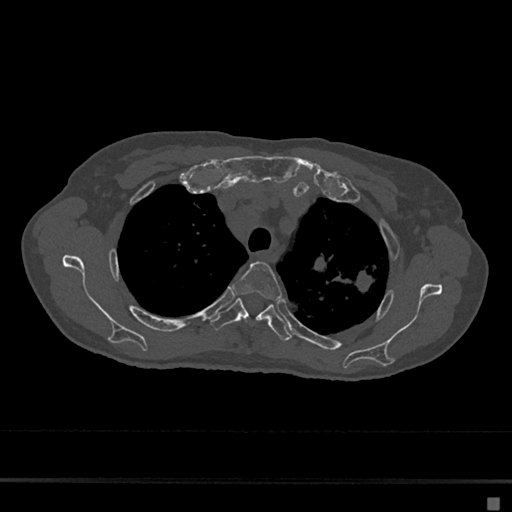
CT including the spine, one axial slice; slice 520 of 797 in the series (ordered by position); 120 kVp; bone window (W 1800 / L 400 HU); 512 × 512 image matrix, field of view 360 × 360 mm. Female patient, age 68 years. Case-level facts recorded for this patient, not image findings: primary cancer: renal.
Annotated regions visible in this slice (semi-automatic segmentation, software-assisted and operator-edited):
- T3 vertebra: bounding box [x1, y1, x2, y2] px = [231, 262, 282, 301]
- T4 vertebra: [210, 299, 291, 341]